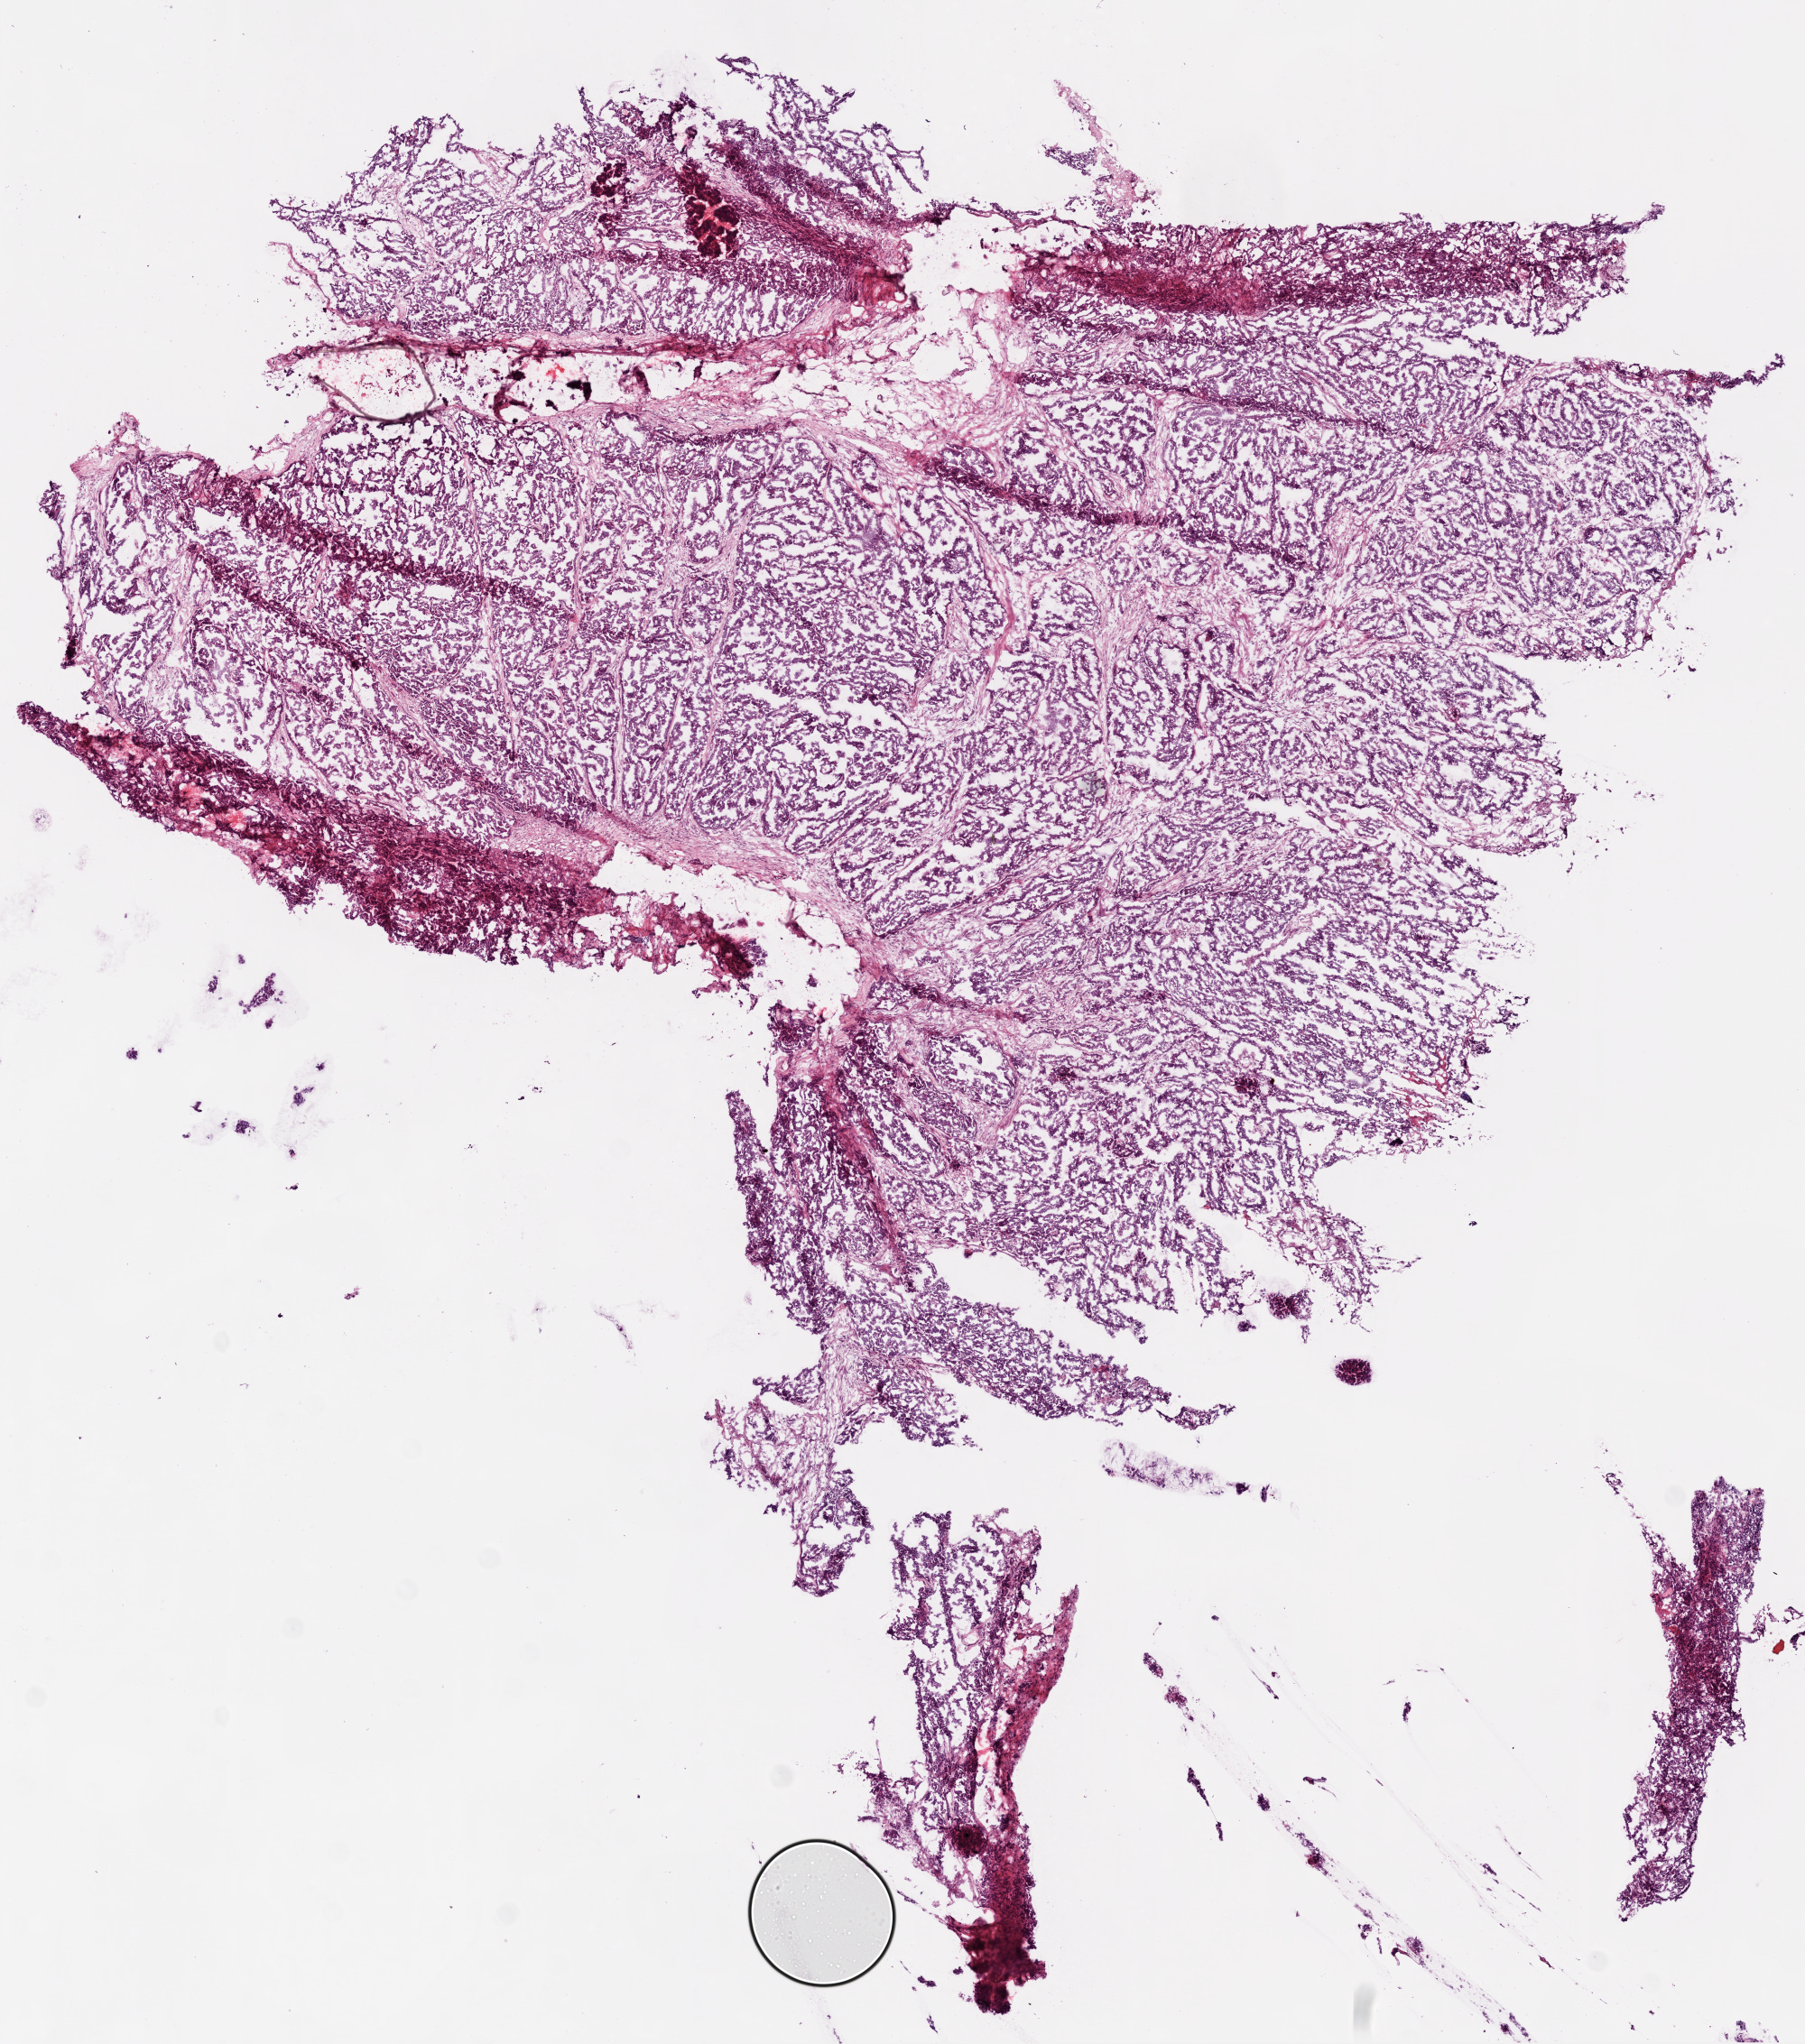
H&E-stained whole-slide image, a low-resolution overview of the entire scanned area, about 8.0 x 9.1 mm (from a 20x scan); frozen section from the bottom of the tissue portion; sample: primary tumour, ovary. Female, age 57 years at initial diagnosis. Histologic grade: G3 (poorly differentiated). Slide review estimates, as recorded: tumour cells 90%, tumour nuclei 95%, normal cells 0%, stromal cells 8%, necrosis 2%.
• laterality: right
• pathologic diagnosis: Serous cystadenocarcinoma, NOS
• FIGO stage: IIIC